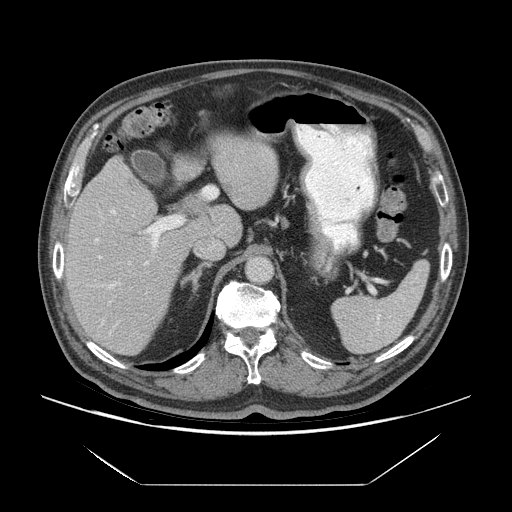
Contrast-enhanced abdominal CT (liver protocol), one axial slice; slice 41 of 75 in the series (ordered by position); reconstruction kernel STANDARD; soft-tissue window (W 400 / L 40 HU); 2.5 mm slice thickness; 512 × 512 image matrix, field of view 420 × 420 mm. From the clinical record (not read from this slice): diagnosis: hepatocellular carcinoma (patient treated with transarterial chemoembolisation; whether this scan precedes or follows treatment is not stated here); TNM stage (as recorded): Stage-I; Child-Pugh class: A; tumour differentiation: well differentiated; tumour size: 5.8 cm.
Outlined on this slice (semi-automatically segmented with operator editing):
- liver parenchyma outside the tumour (the mass and vessels are separate outlines, so this box may not span the whole liver): box from (x=66, y=156) to (x=242, y=354) px
- liver vessels: (x=95, y=209)–(x=185, y=334)